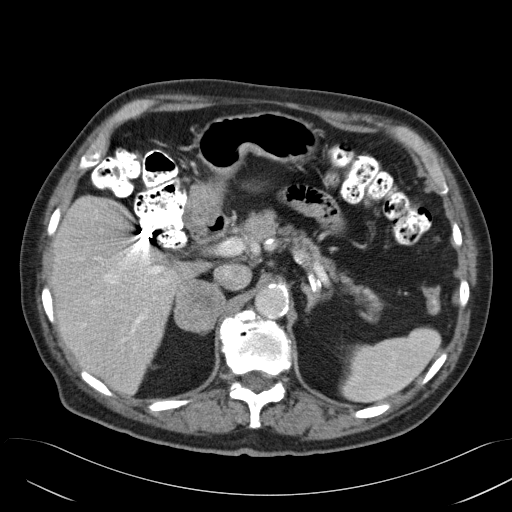
Contrast-enhanced abdominal CT, one axial slice; position 33 of 58 along the scan axis; reconstruction kernel B31f; 120 kVp; intravenous contrast given; soft-tissue window (W 400 / L 40 HU); 5 mm slice thickness; 512 × 512 image matrix, field of view 384 × 384 mm. Male patient, age 82 years. From the clinical record (not read from this slice): diagnosis: adrenocortical carcinoma; tumour side: right adrenal; tumour size at pathology: 9 cm; Ki-67 index: 30 %; stage (as recorded): 3.
Outlined on this slice (semi-automatic segmentation, software-assisted and operator-edited):
- mass: box from (x=174, y=279) to (x=225, y=334) px